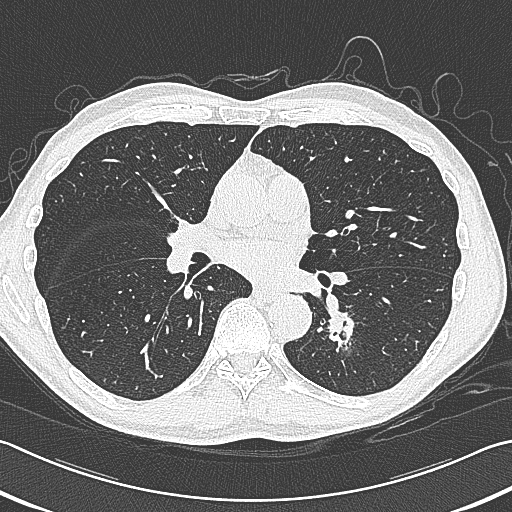
Low-dose screening chest CT, axial slice; first (baseline) screen; lung window (W 1500 / L -600 HU); 1 mm slice thickness; lung (sharp) reconstruction kernel (B80f); slice 172 of 354 in the series. Male participant, aged 59 years at enrolment.
Expert reader's lesion annotation, bounding box (x1, y1, x2, y2) in pixels: (313, 294, 375, 353). The exam's reader record, not a measurement of the box and not confirmed to be the same lesion: non-calcified nodule or mass ≥4 mm, left lower lobe, 15 × 15 mm, smooth margins, soft tissue attenuation. Official screen result: positive, change unspecified: nodule(s) >= 4 mm or enlarging nodule(s), mass(es), or other non-specific abnormalities suspicious for lung cancer. Lung cancer was diagnosed 17 days after this screen: squamous cell carcinoma, large cell, nonkeratinizing, NOS, left lower lobe, poorly differentiated (G3), stage IB (AJCC 6th edition), 31 mm at pathology.